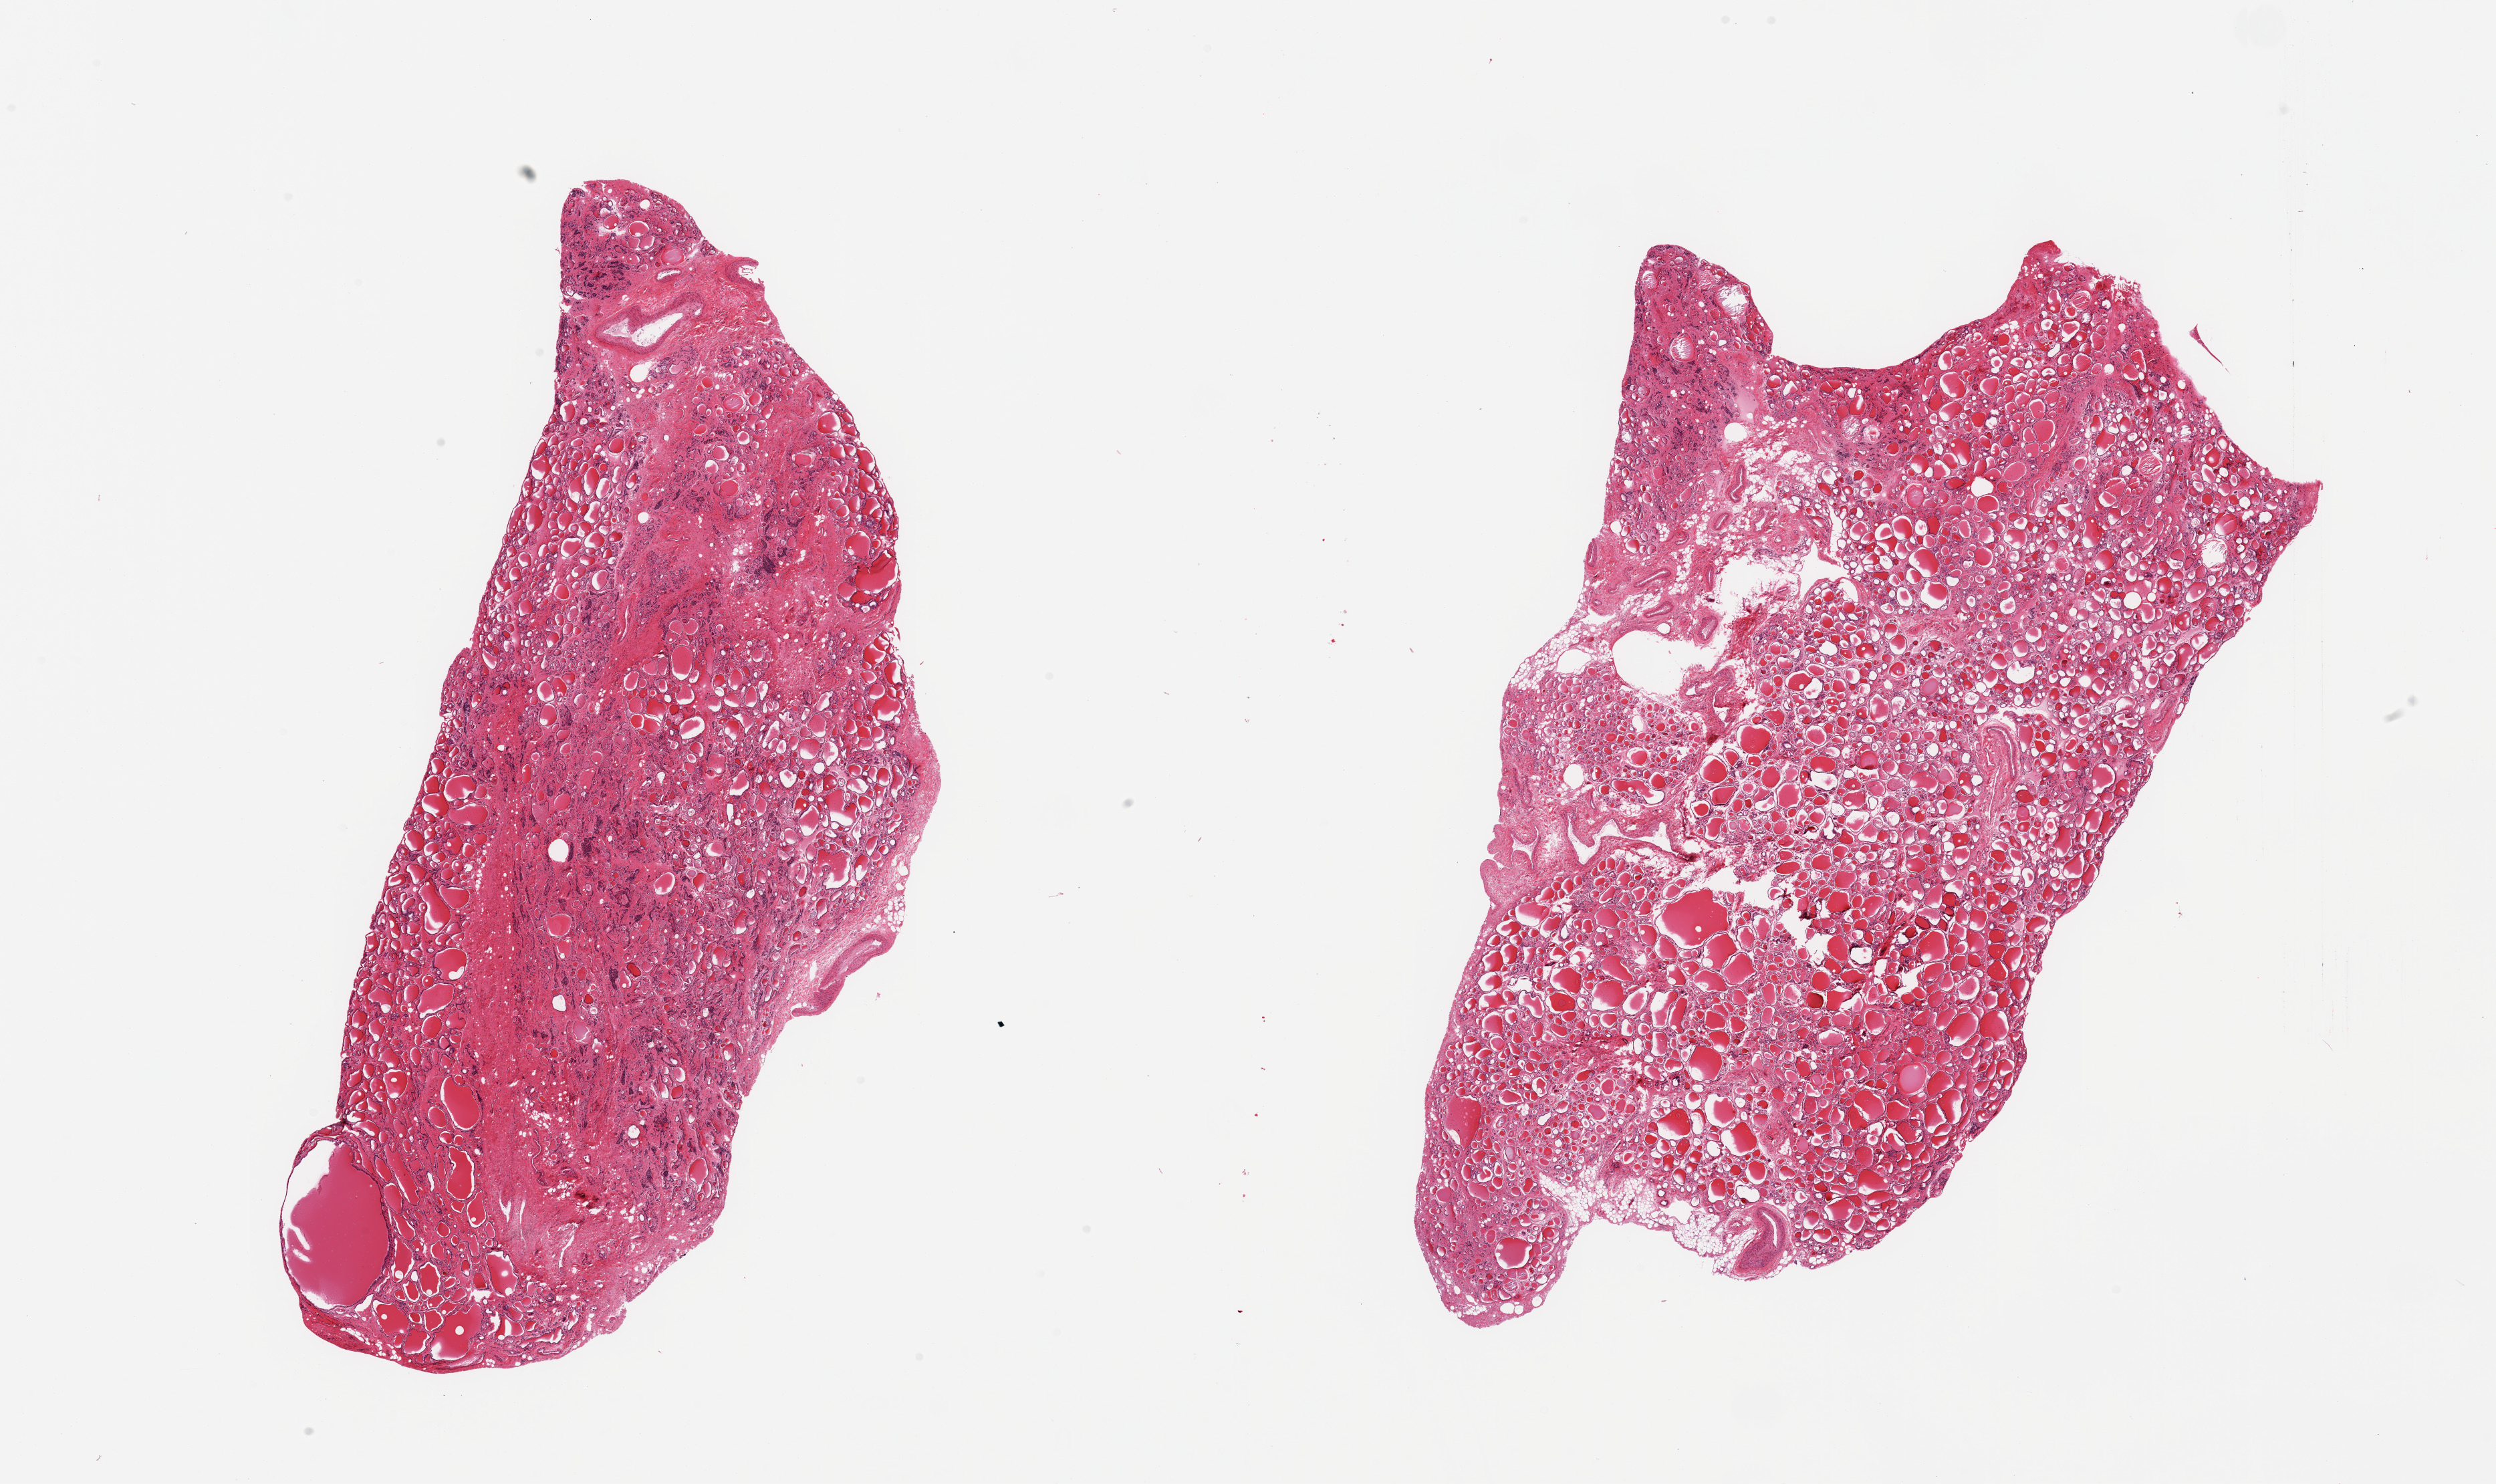
Hematoxylin and eosin (H&E) whole-slide image — shown as a low-resolution overview of the whole scanned area (about 29.5 x 17.6 mm); PAXgene-fixed paraffin-embedded (PFPE) section; sampled site (target tissue): thyroid; donor tissue sample. Donor: male.
Reviewer comment on this tissue sample: 2 pieces, no abnormalities.